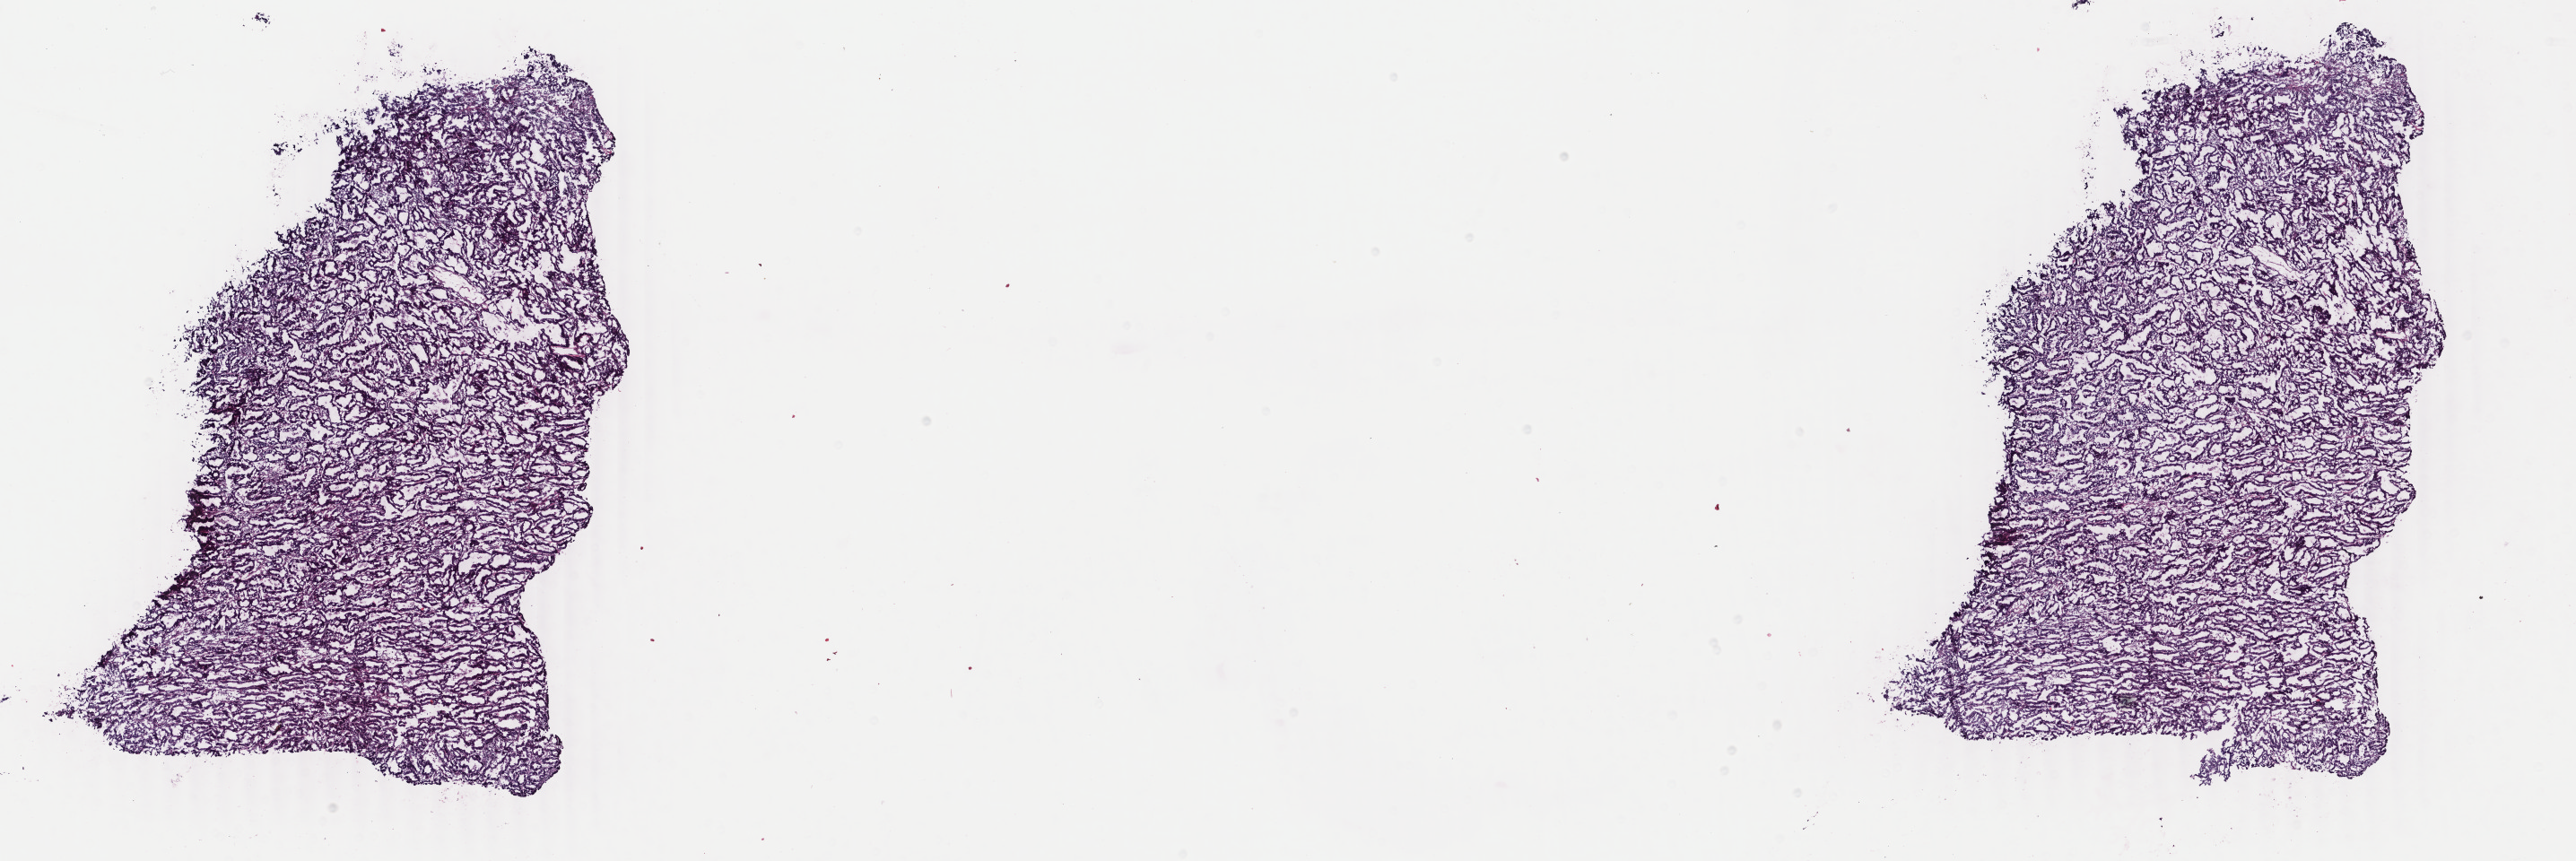
Digitized H&E tissue section (whole slide) — whole scanned area (about 22.8 x 7.6 mm, slide scanned at 40x) shown as a low-resolution overview. Frozen section from the bottom of the tissue portion. Uterus, primary tumour sample. Female, age 64 years at initial diagnosis. Histologic grade: G1 (well differentiated). Slide review estimates, as recorded: tumour cells 100%, tumour nuclei 85%, normal cells 0%, stromal cells 0%, necrosis 0%. Inflammatory infiltration, as recorded: lymphocyte infiltration 0%, monocyte infiltration 0%, neutrophil infiltration 0%.
• pathologic diagnosis: Endometrioid adenocarcinoma, NOS (endometrium)
• FIGO stage: IA